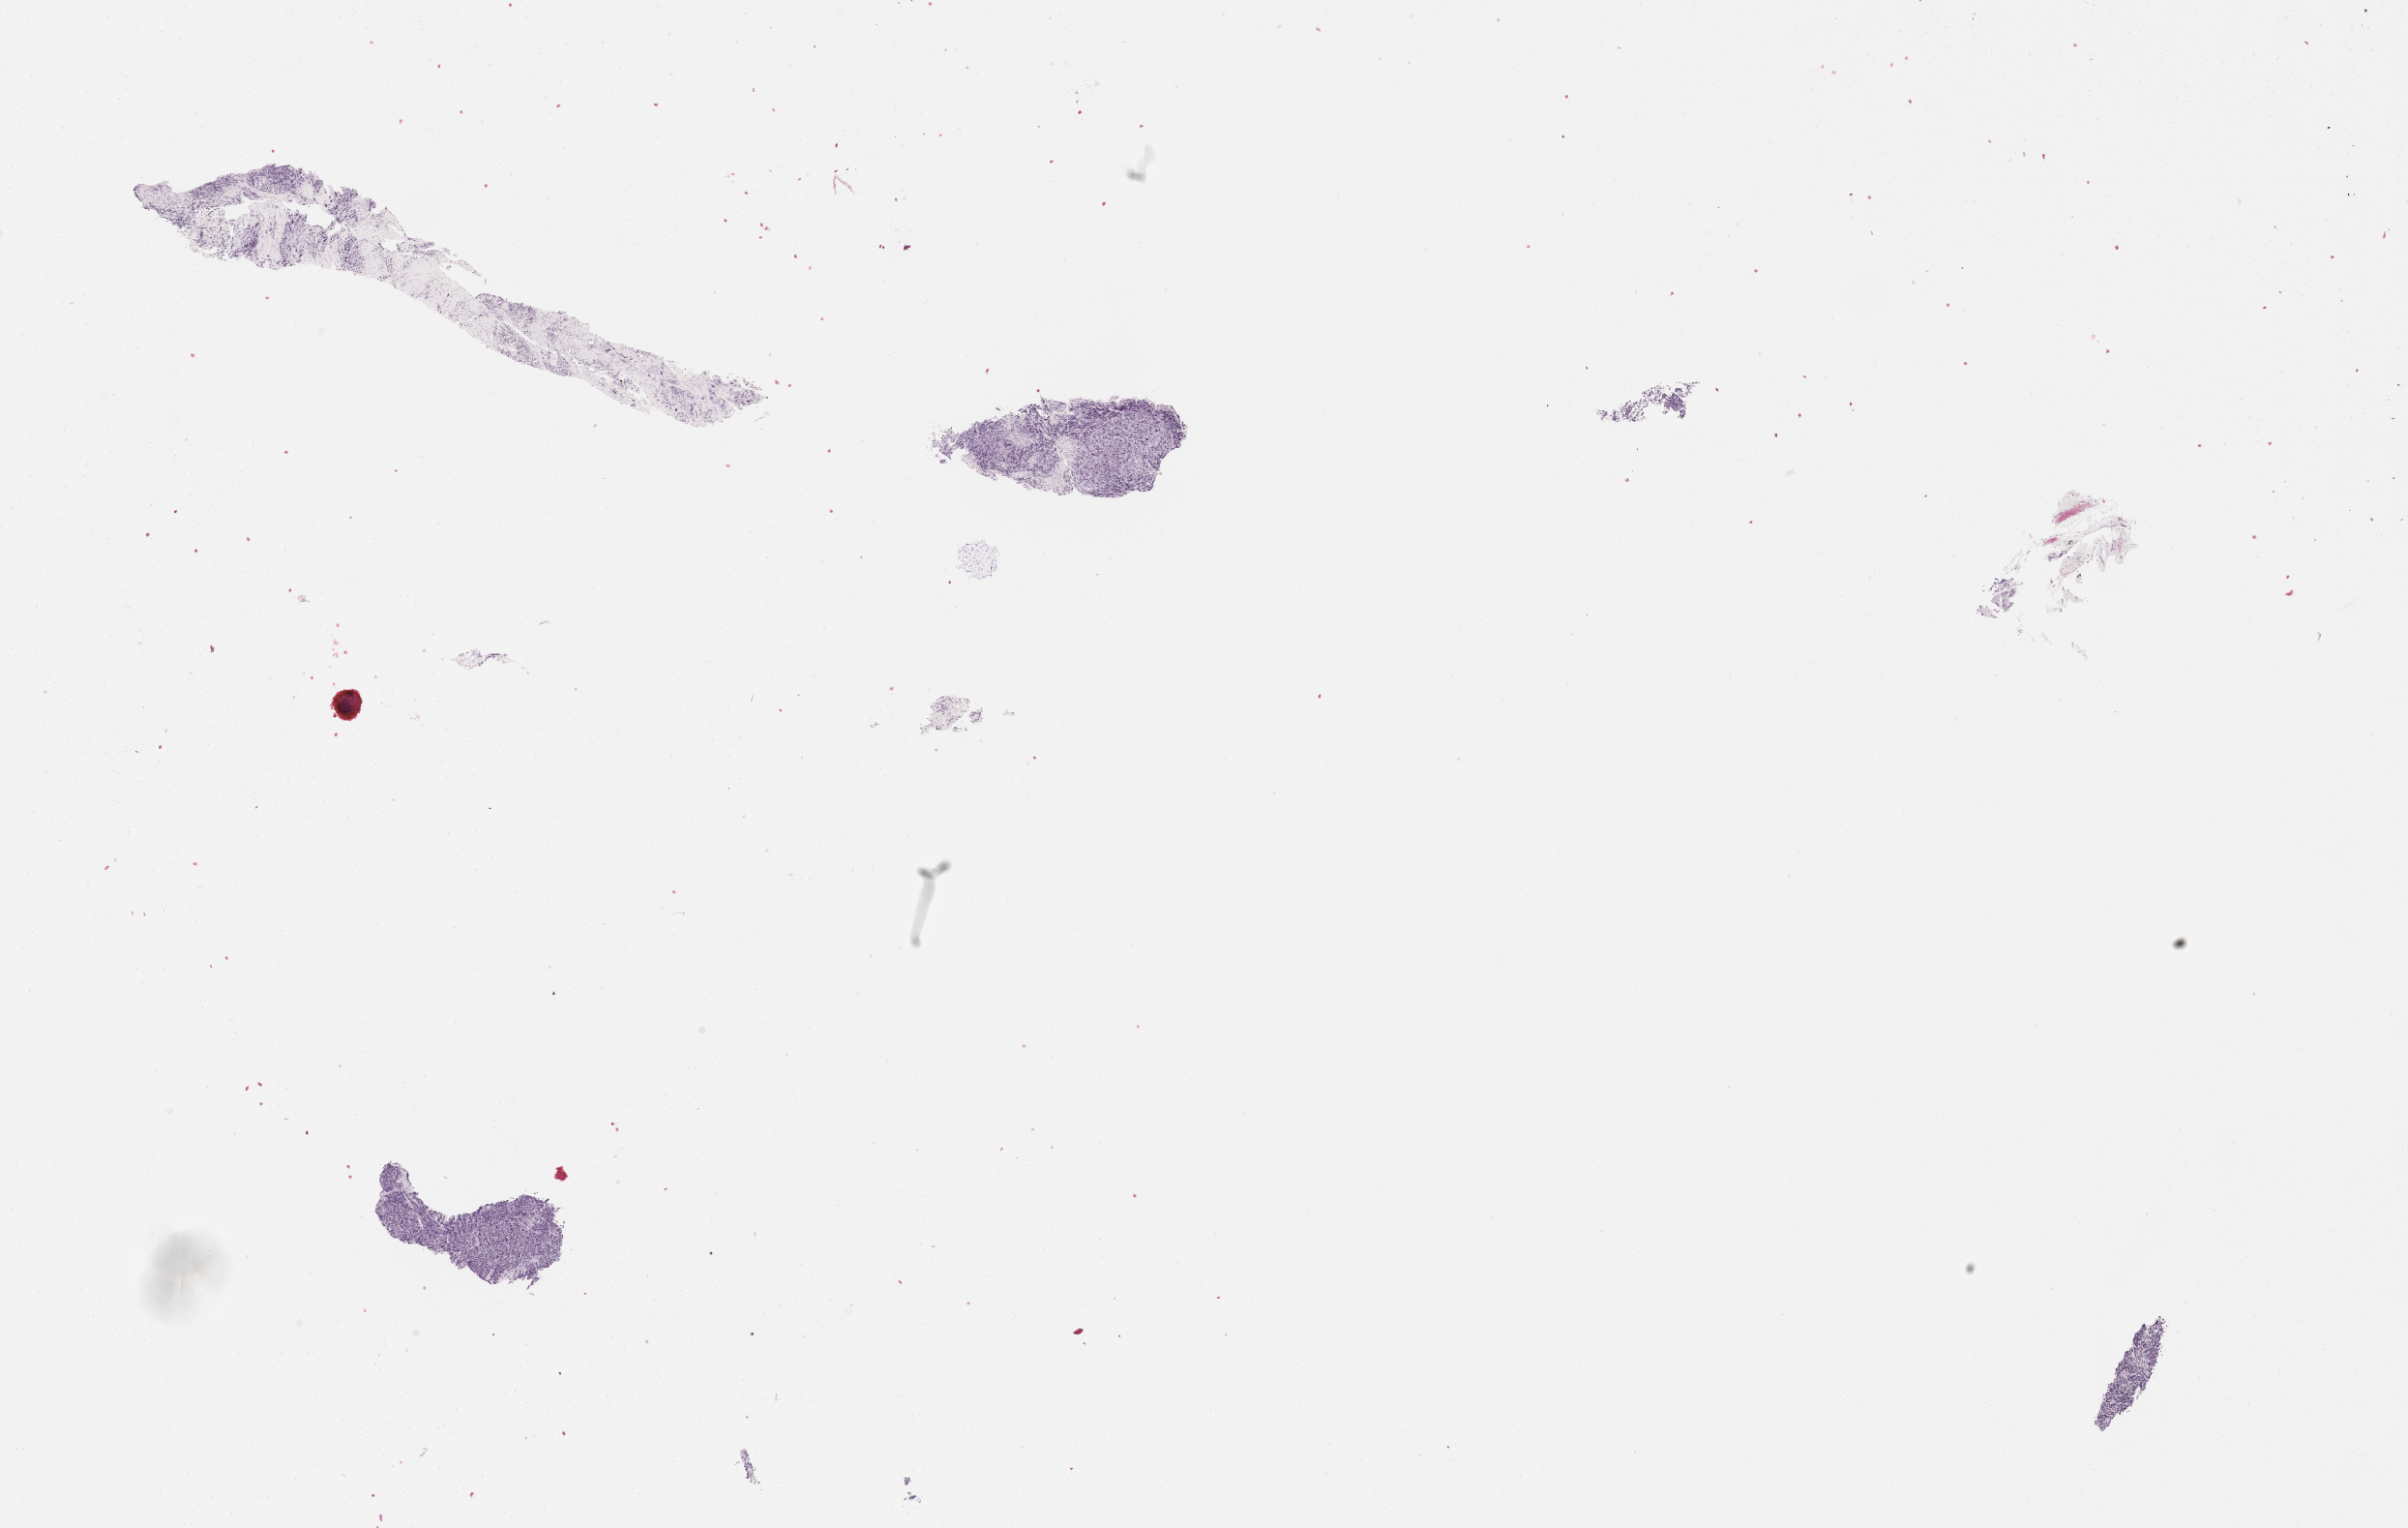
Hematoxylin and eosin (H&E) whole-slide image of tumor tissue — a low-resolution overview of the entire scanned area, about 20.1 x 12.8 mm, formalin-fixed paraffin-embedded section, site: soft tissue, thigh-right posterior. Male patient, age at diagnosis 2.4 years.
Stage (as recorded): 3. Diagnosis: rhabdomyosarcoma; histological classification: embryonal rhabdomyosarcoma. Metastatic status at presentation (as recorded): non-metastatic (confirmed).